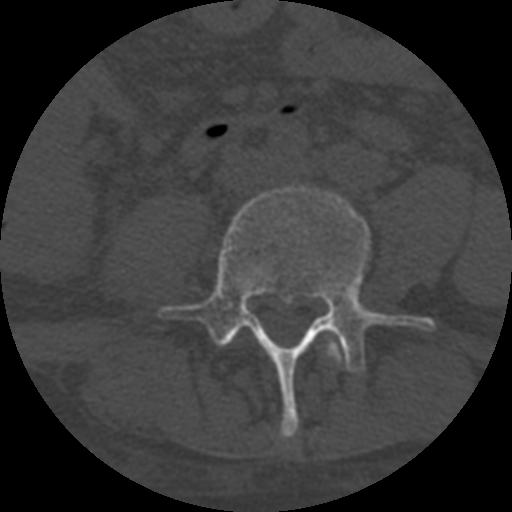
CT including the spine, one axial slice; position 212 of 708 along the scan axis; reconstruction kernel STANDARD; one of 3 acquisitions stored at this slice position; bone window (W 1800 / L 400 HU); 1.25 mm slice thickness; 512 × 512 image matrix, field of view 160 × 160 mm. Patient age 55 years. Case-level facts recorded for this patient, not image findings: primary cancer: colon.
Outlined on this slice (semi-automatic segmentation, software-assisted and operator-edited):
- L3 vertebra: bounding box [x1, y1, x2, y2] px = [326, 341, 342, 363]
- L4 vertebra: [159, 186, 436, 438]